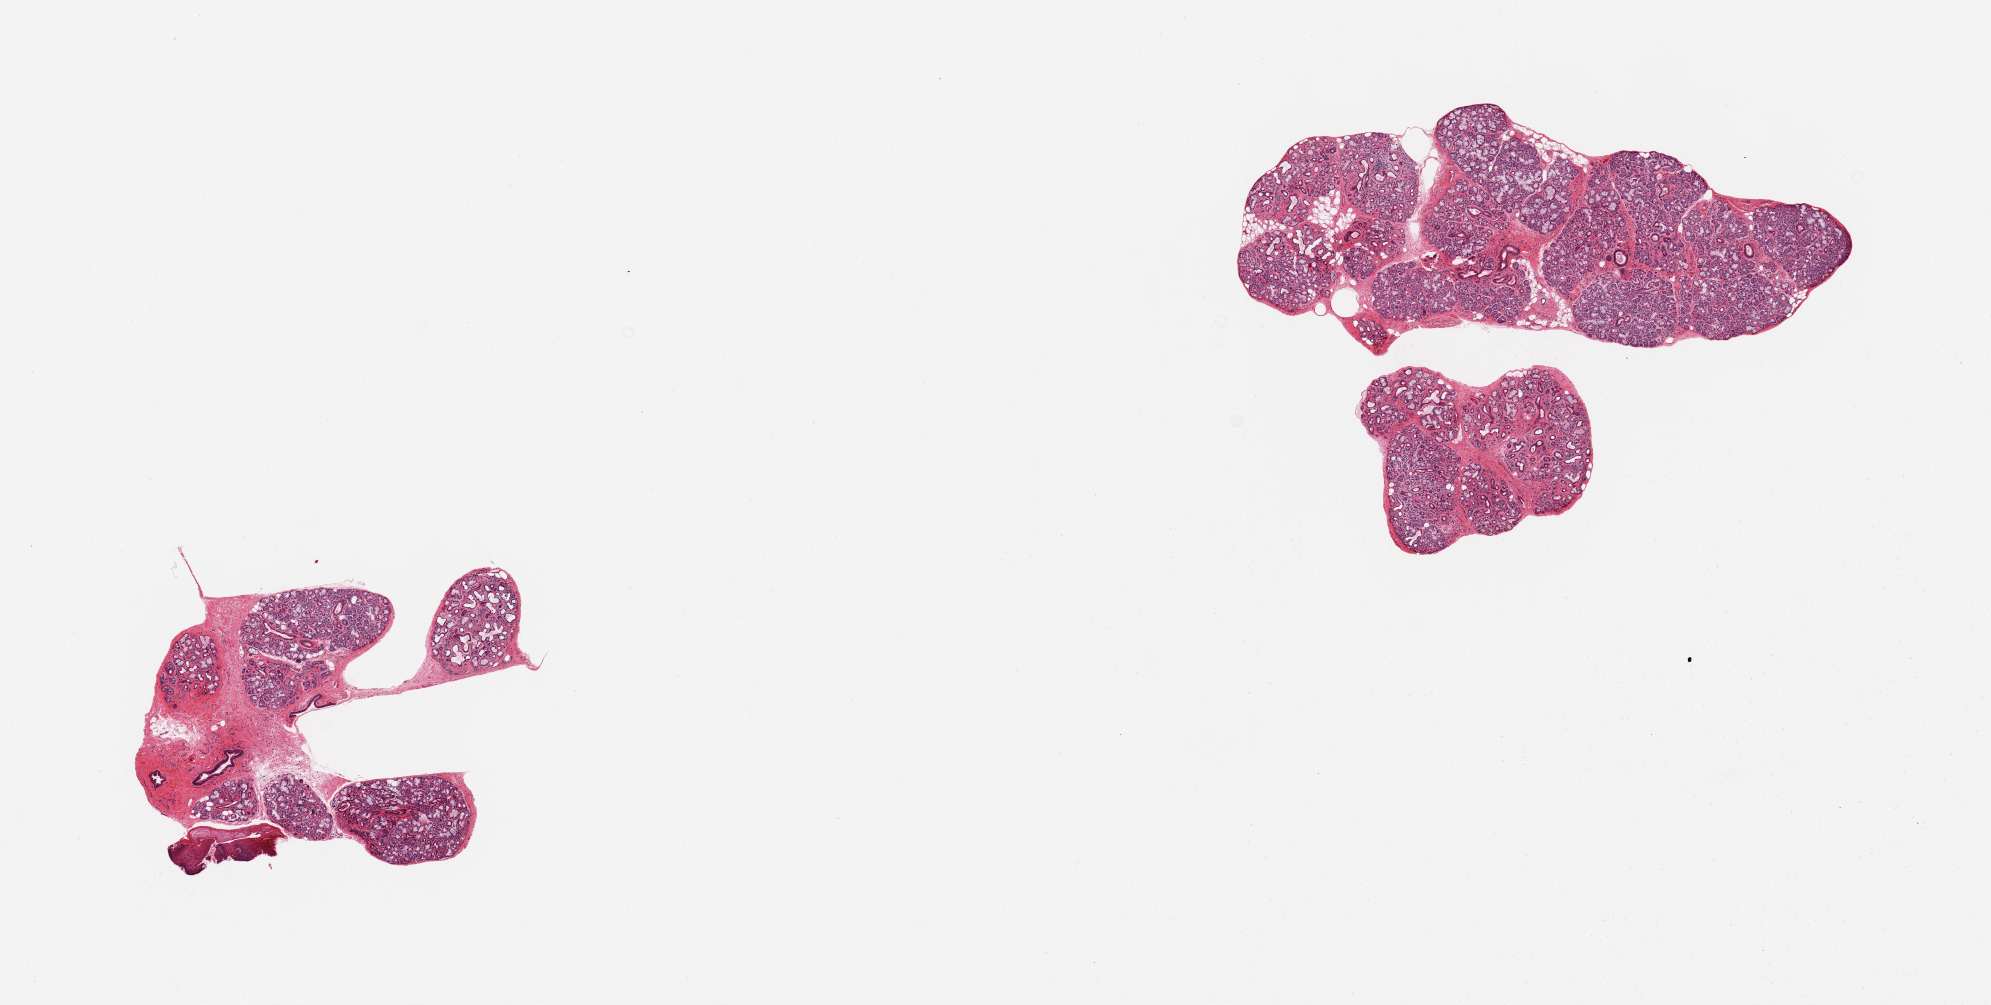
Digitized hematoxylin and eosin (H&E)-stained section — a low-resolution overview of the entire scanned area, about 15.8 x 8.0 mm (from a 20x scan); PAXgene-fixed paraffin-embedded (PFPE) section; section of minor salivary gland (target tissue); tissue donor sample. Donor: male.
Reviewer comment on this tissue sample: 2 pieces, ~80% glandular elements, good specimen.